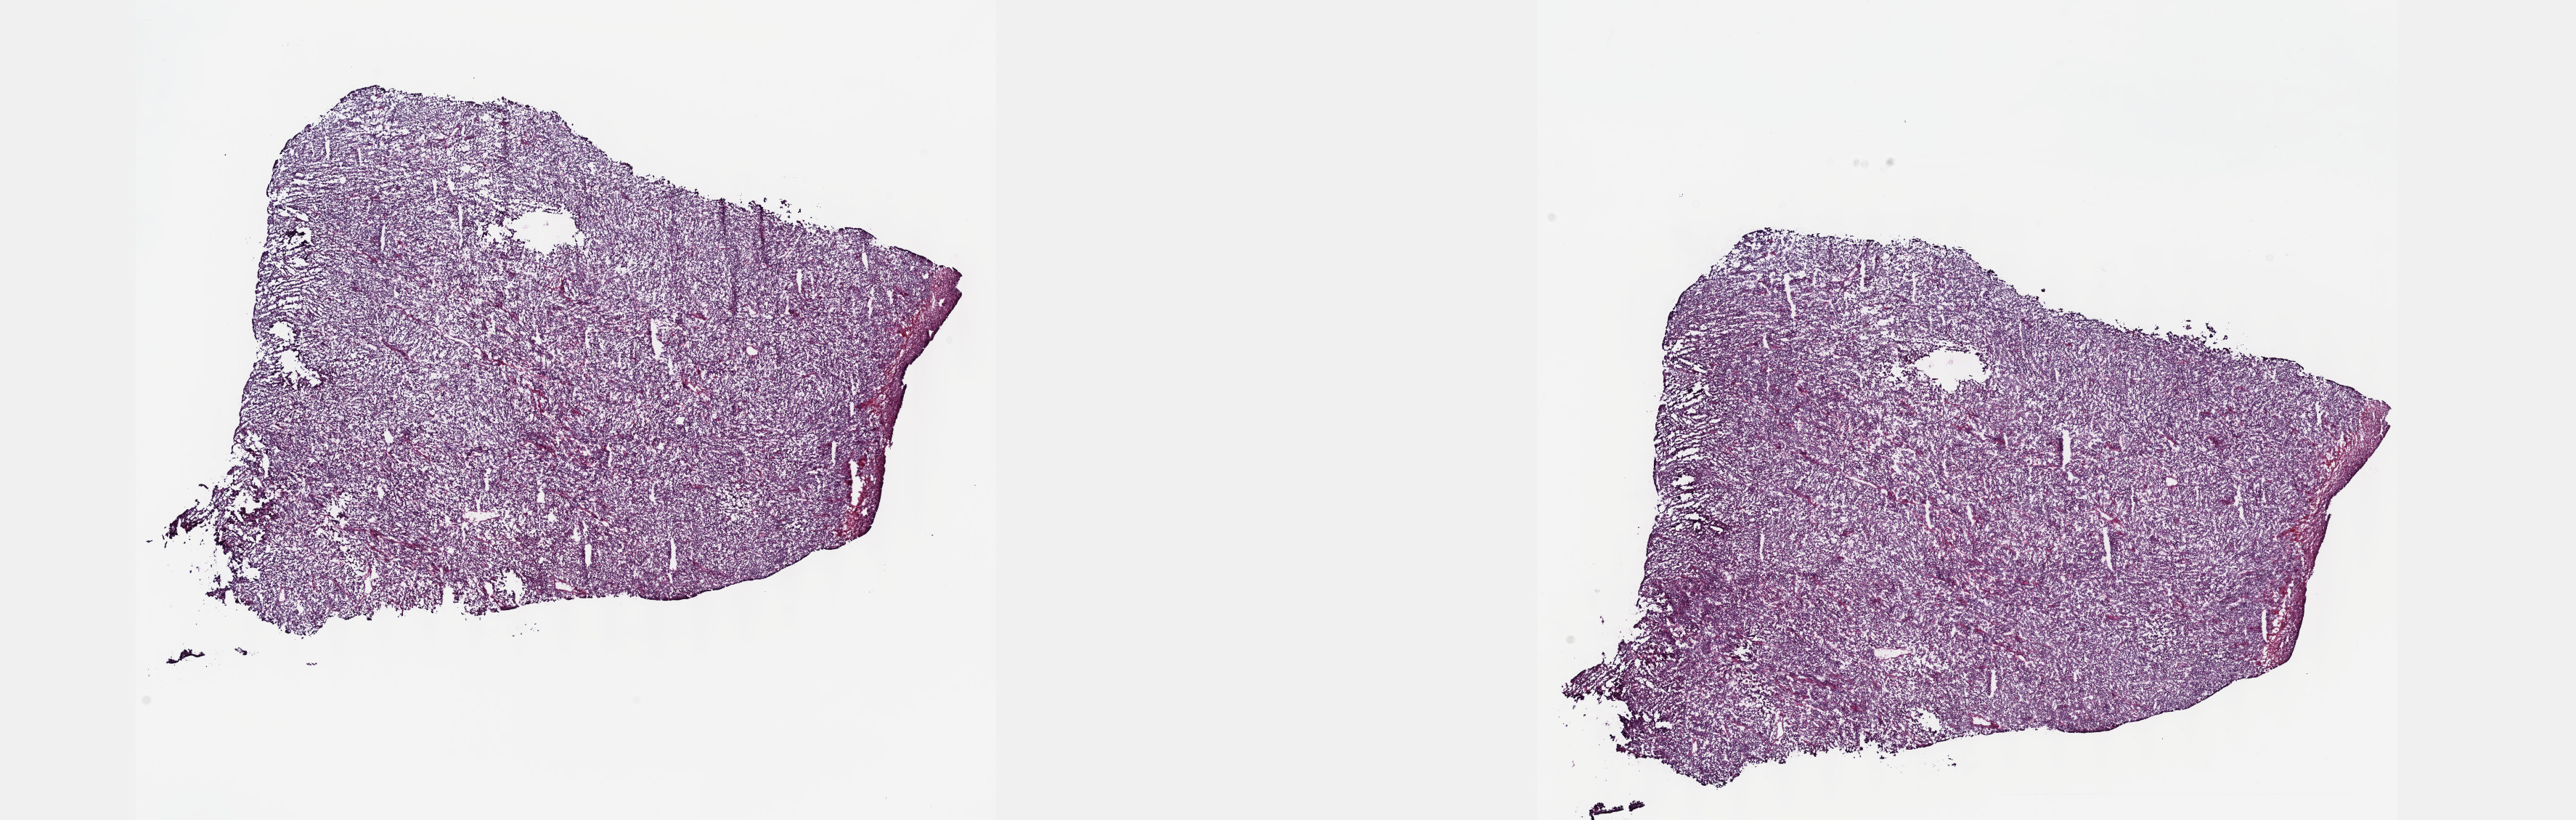
Digitized Hematoxylin and eosin (H&E) stained tissue section (whole slide) — shown as a low-resolution overview of the whole scanned area (about 28.7 x 9.1 mm, from a 40x scan), frozen section from the top of the tissue portion, metastatic tumour sample. Male patient; age at initial diagnosis 66 years. Composition of this section per pathologist review: tumour cells 100%, tumour nuclei 92%, normal cells 0%, stromal cells 0%, necrosis 0%. Infiltration values recorded for this section: lymphocyte infiltration 0%, monocyte infiltration 0%, neutrophil infiltration 0%.
This section: metastatic tumour tissue. Patient diagnosis: Malignant melanoma, NOS.